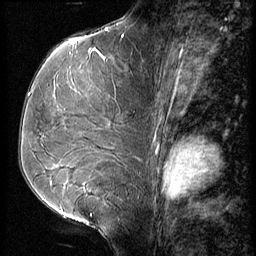
Breast MRI (dynamic contrast-enhanced), one sagittal slice. Slice 33 of 56 in the series (ordered by position). 3 images stored at this slice position (order not interpretable as contrast timing). 1.5 T. TE 4.2 ms, TR 9 ms. 2.5 mm slice thickness. 256 × 256 image matrix, field of view 180 × 180 mm. Patient: female, 51 years. Case-level facts recorded for this patient, not image findings: setting: breast cancer imaged before/during neoadjuvant chemotherapy; receptor status: HR-positive, HER2-negative.
Outlined on this slice (semi-automatically segmented with operator editing):
- analysis volume of interest (the breast-tissue region the enhancement analysis was run in; not a lesion): bounding box (x1, y1, x2, y2) in pixels: (23, 56, 151, 165)
- tumour enhancement mask (voxels above the 140 % enhancement threshold inside the analysis volume of interest): (29, 58, 105, 95)